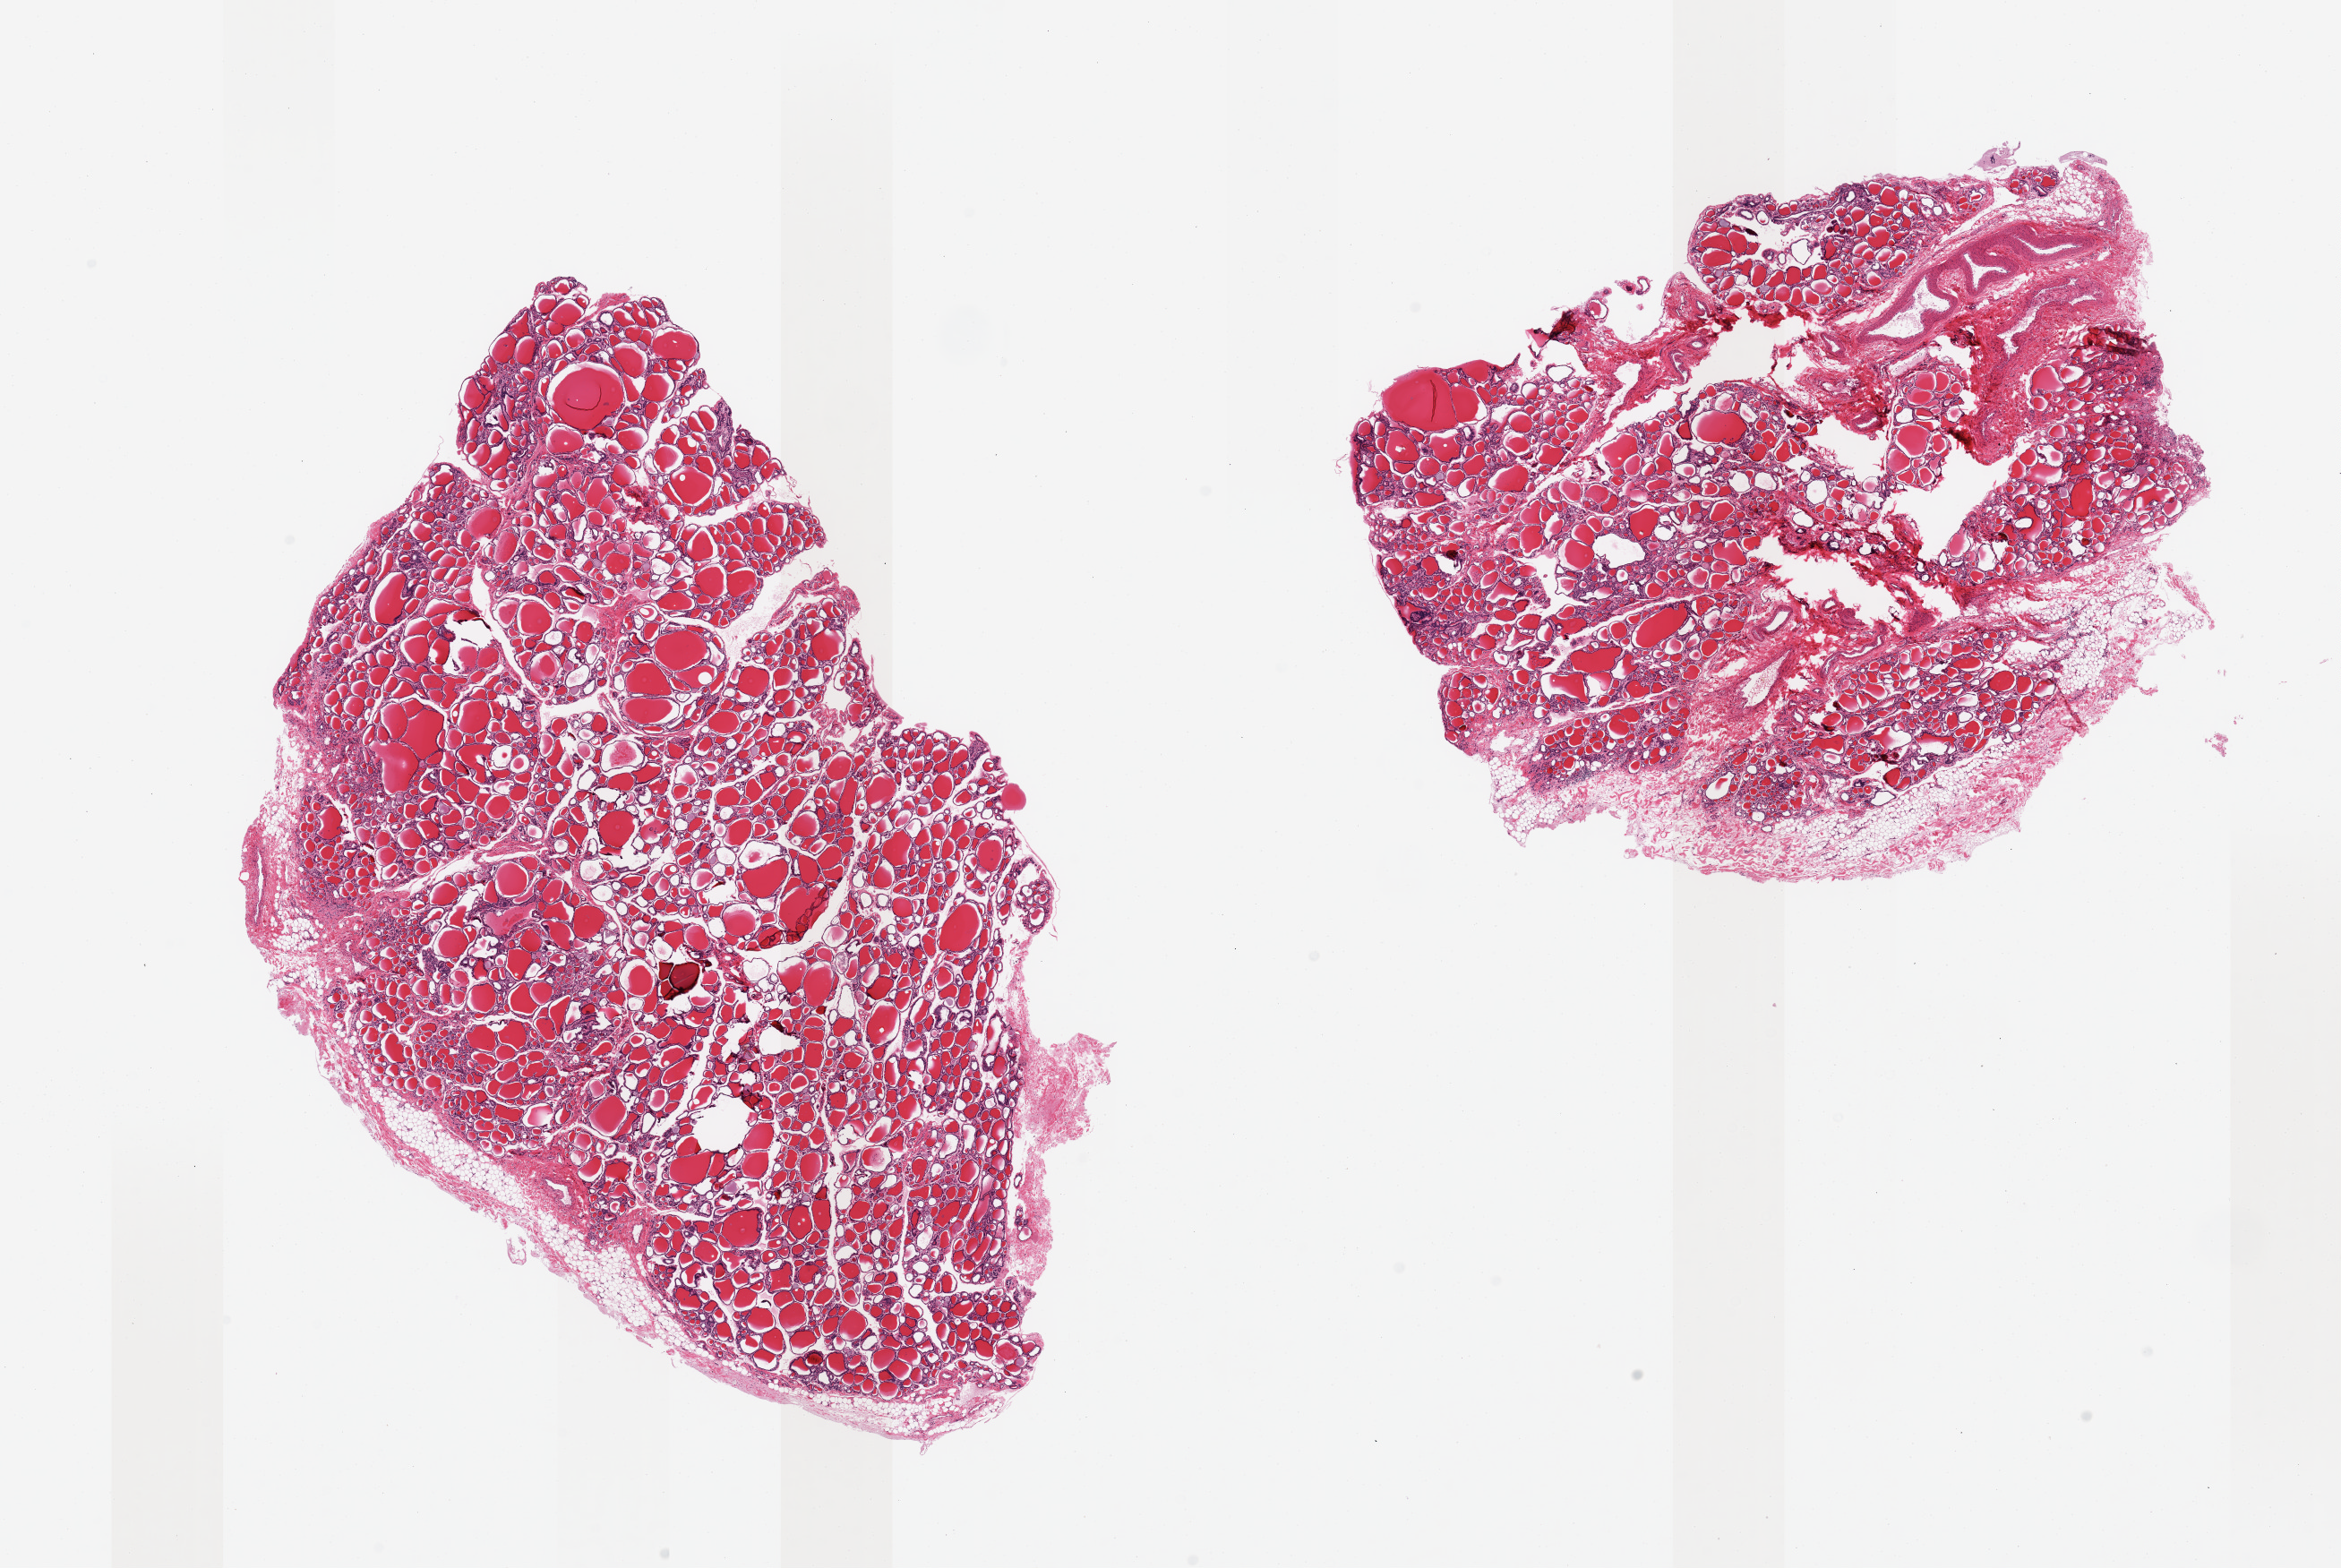
Haematoxylin and eosin whole-slide image — whole scanned area (about 20.7 x 13.8 mm, slide scanned at 20x) shown as a low-resolution overview; PAXgene-fixed paraffin-embedded (PFPE) section; sampled site (target tissue): thyroid; tissue donor sample. Donor: female.
Pathologist's review note for this sample: 2 pieces; no lesions; generally well dissected; some tissue fractures.